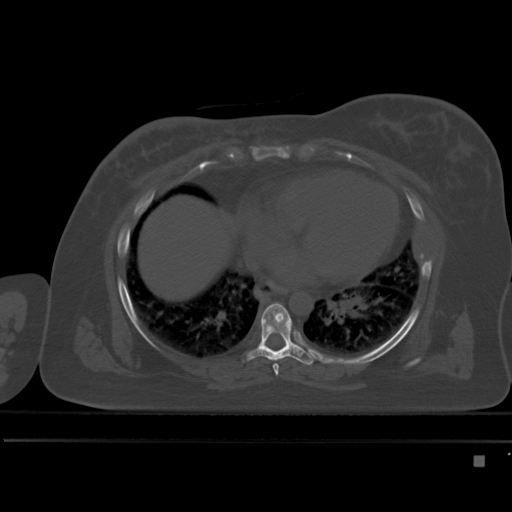
CT including the spine, one axial slice; bone window (W 1800 / L 400 HU); 1.5 mm slice thickness; 512 × 512 image matrix, field of view 404 × 404 mm. Female patient, age 33 years. Case-level facts recorded for this patient, not image findings: primary cancer: breast.
Structures marked on this image (semi-automatically segmented with operator editing):
- T6 vertebra: bounding box <273,364,279,375> (left, top, right, bottom; pixels)
- T7 vertebra: <246,303,315,365>